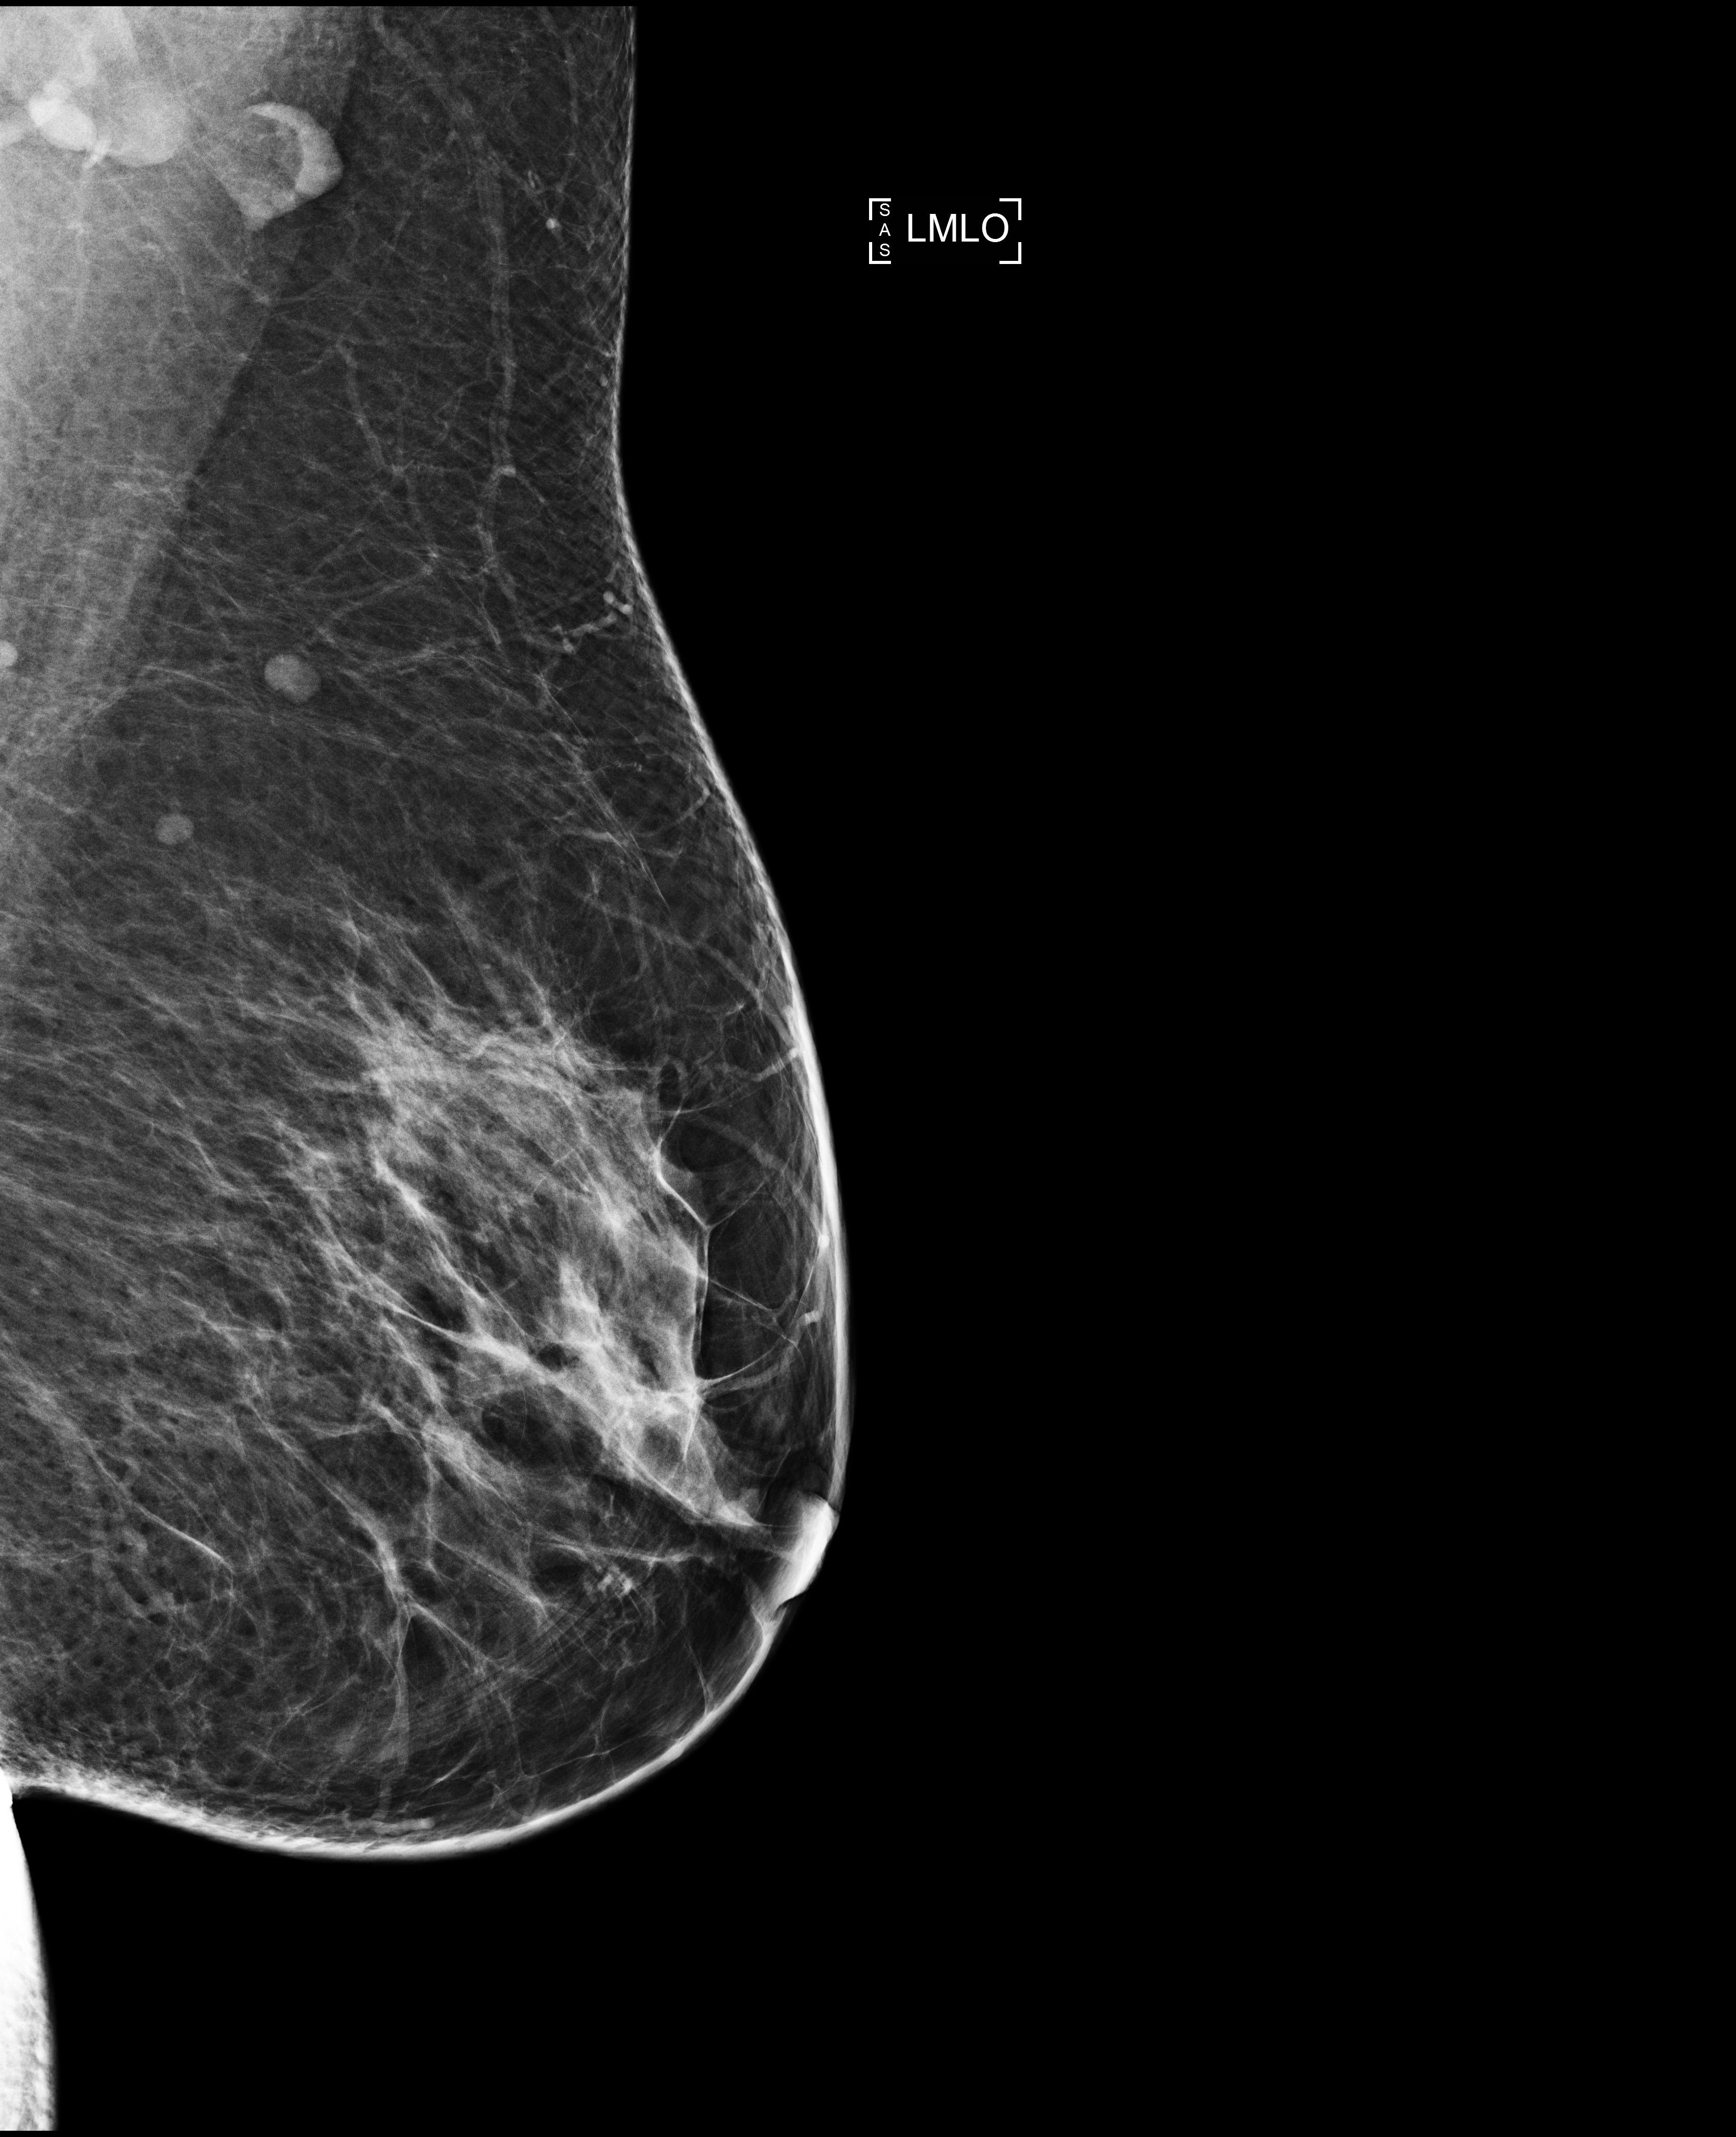
Full-field digital mammogram (FFDM); left breast; mediolateral oblique (MLO) view; screening examination; system: Selenia Dimensions. Female patient, age 46 years.
BI-RADS breast density category at the screening exam (both breasts, scale 1–4): 3. Final BI-RADS category for the screening round (tomosynthesis exam, both breasts): category 1. Recall: no recall after this screen.